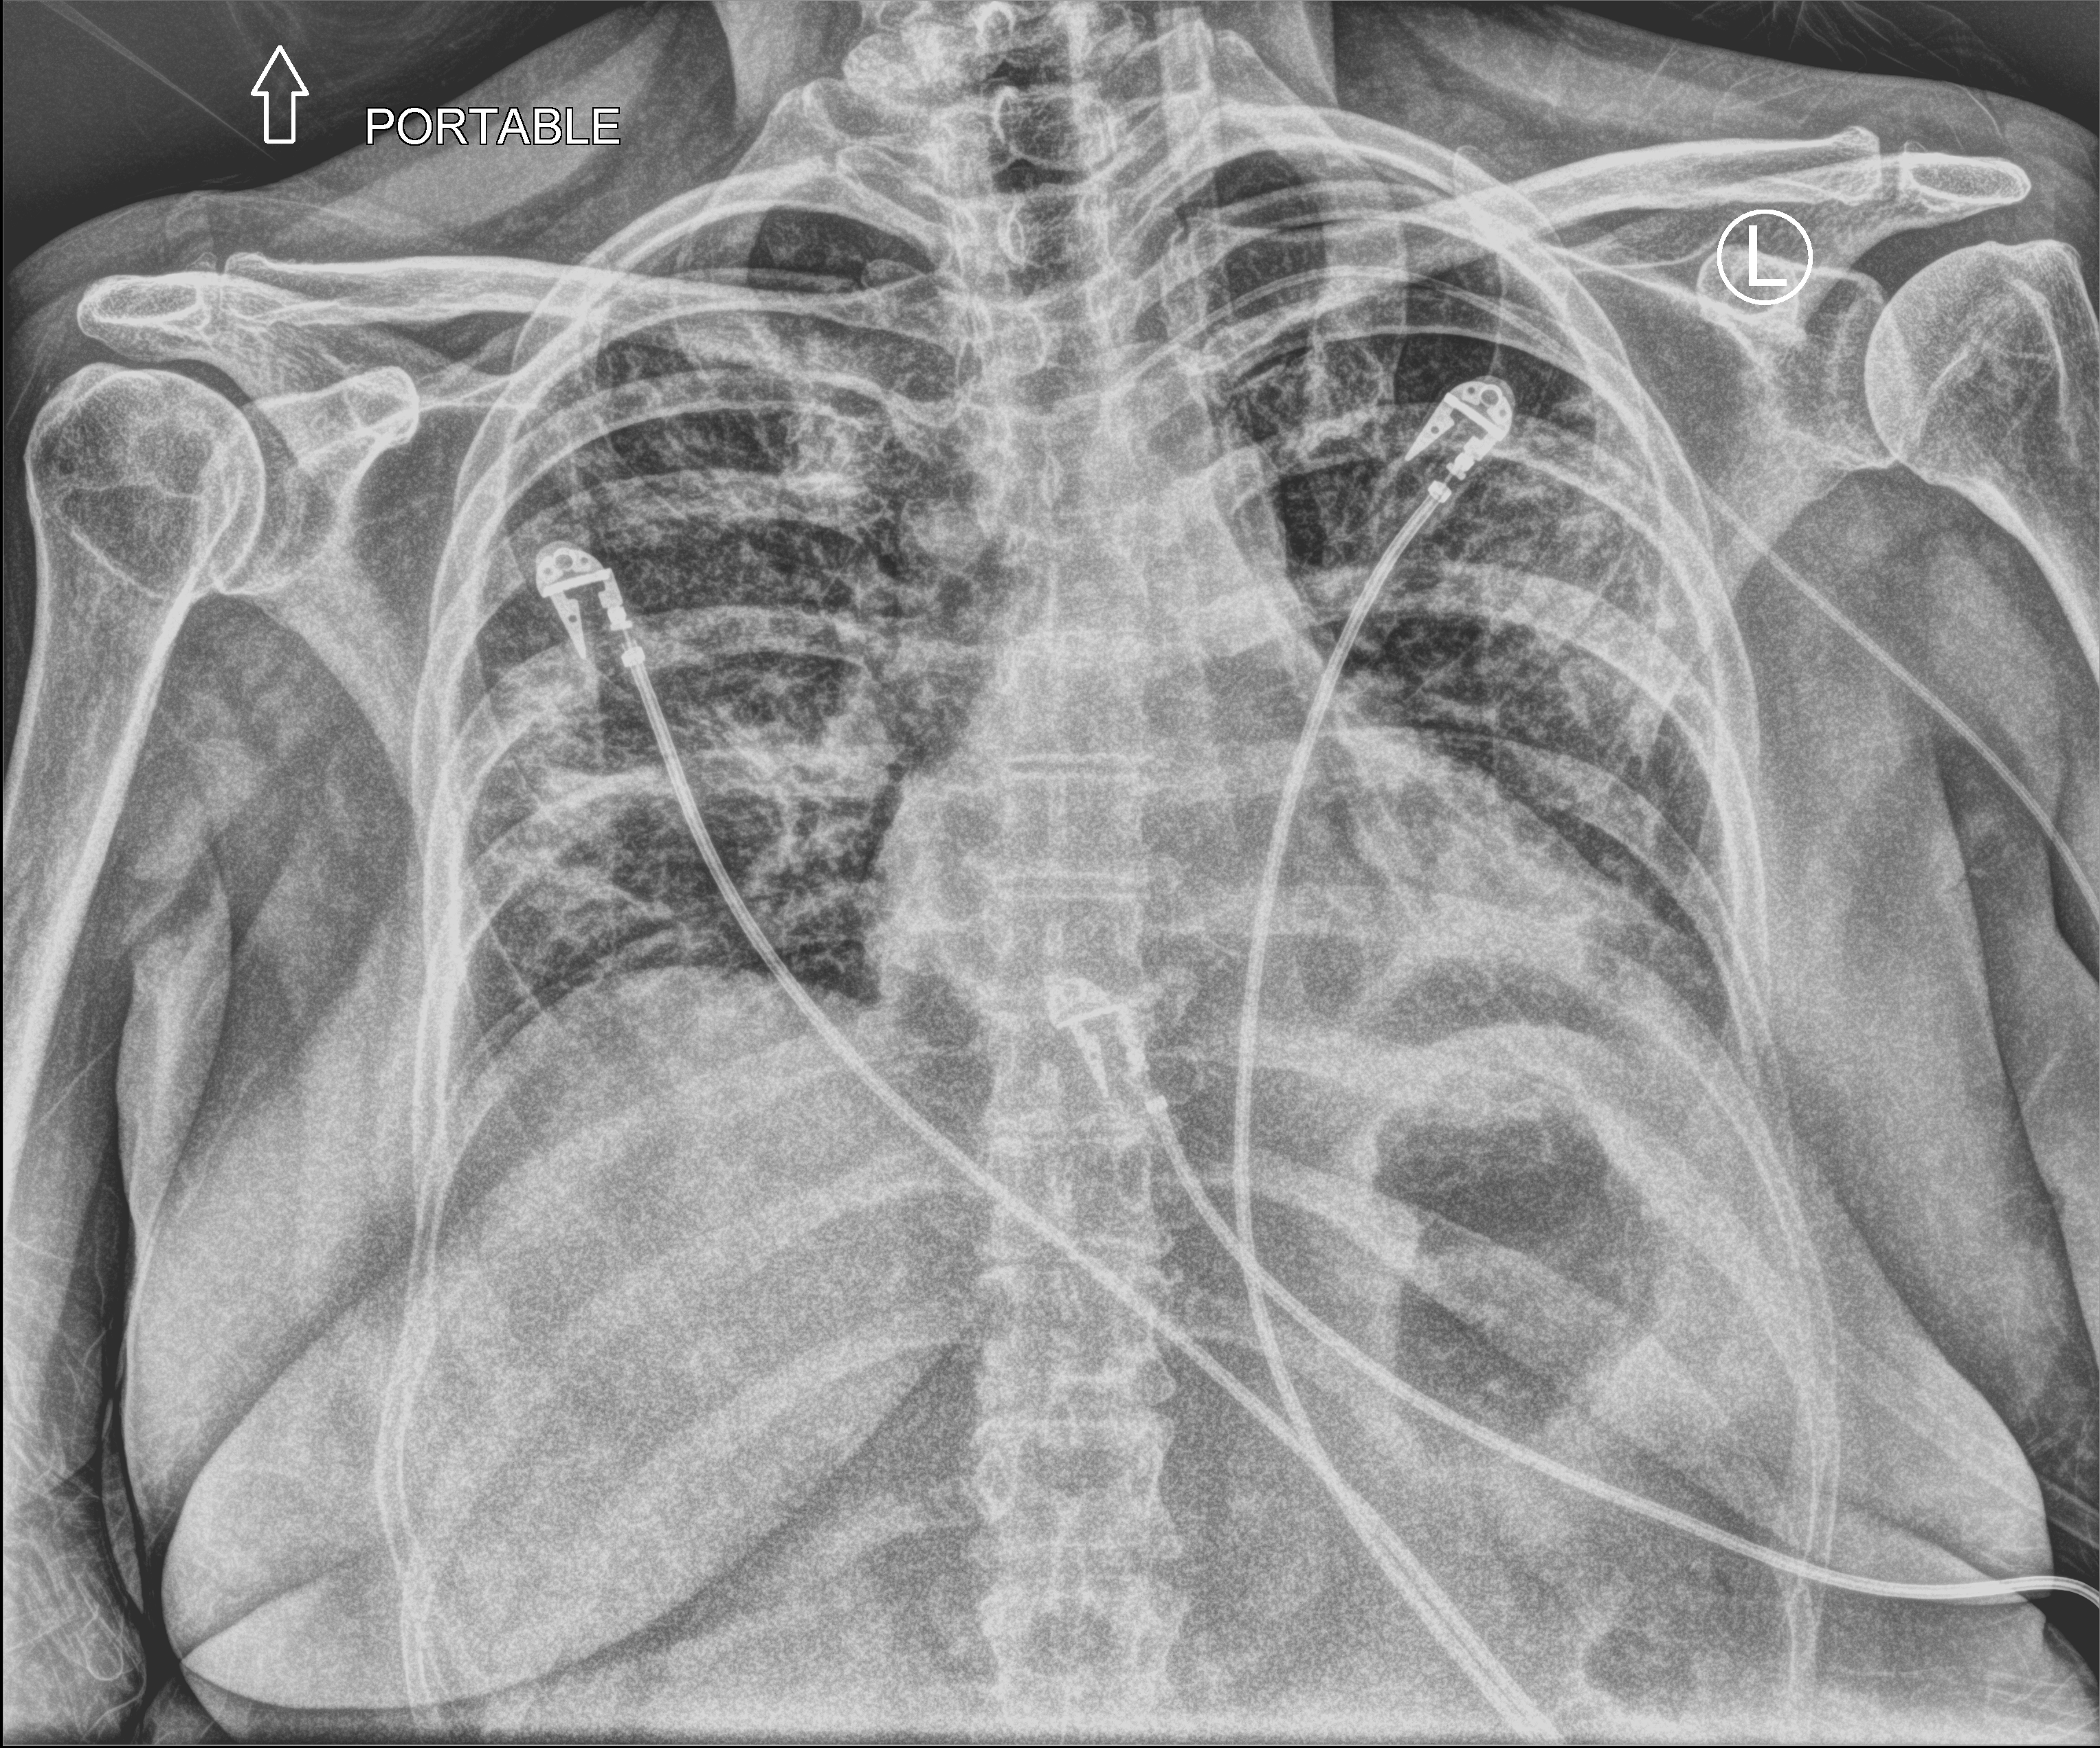
Bedside chest radiograph (computed radiography); anteroposterior (AP) projection. Female patient hospitalised with COVID-19, age 18–59 years.
Admission-level facts for this patient (not findings on this image; timing relative to this image not recorded):
- admitted to intensive care during this hospital stay: yes
- smoking status (admission record): former
- mechanically ventilated during this hospital stay: yes